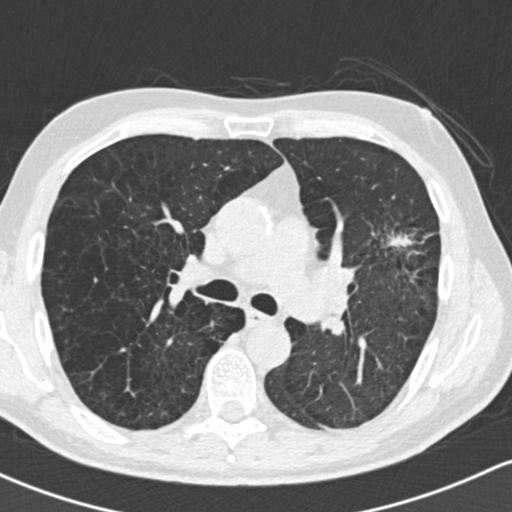
Low-dose screening chest CT, axial slice; baseline screening round; lung window (W 1500 / L -600 HU); standard (soft-tissue) reconstruction kernel (B30f); 120 kVp. Male, age 61 years at enrolment. Former smoker at enrolment.
Expert-annotated lung lesion, bounding box [x1, y1, x2, y2] px = [357, 187, 460, 298]. The exam's reader record, not a measurement of the box and not confirmed to be the same lesion: non-calcified nodule or mass ≥4 mm, left upper lobe, 35 × 35 mm, spiculated (stellate) margins, soft tissue attenuation. Official screen result: positive, change unspecified: nodule(s) >= 4 mm or enlarging nodule(s), mass(es), or other non-specific abnormalities suspicious for lung cancer. Later outcome: lung cancer diagnosed 19 days after this screen — adenocarcinoma, NOS, left upper lobe, well differentiated (G1), stage IIIA (AJCC 6th edition), 45 mm at pathology.